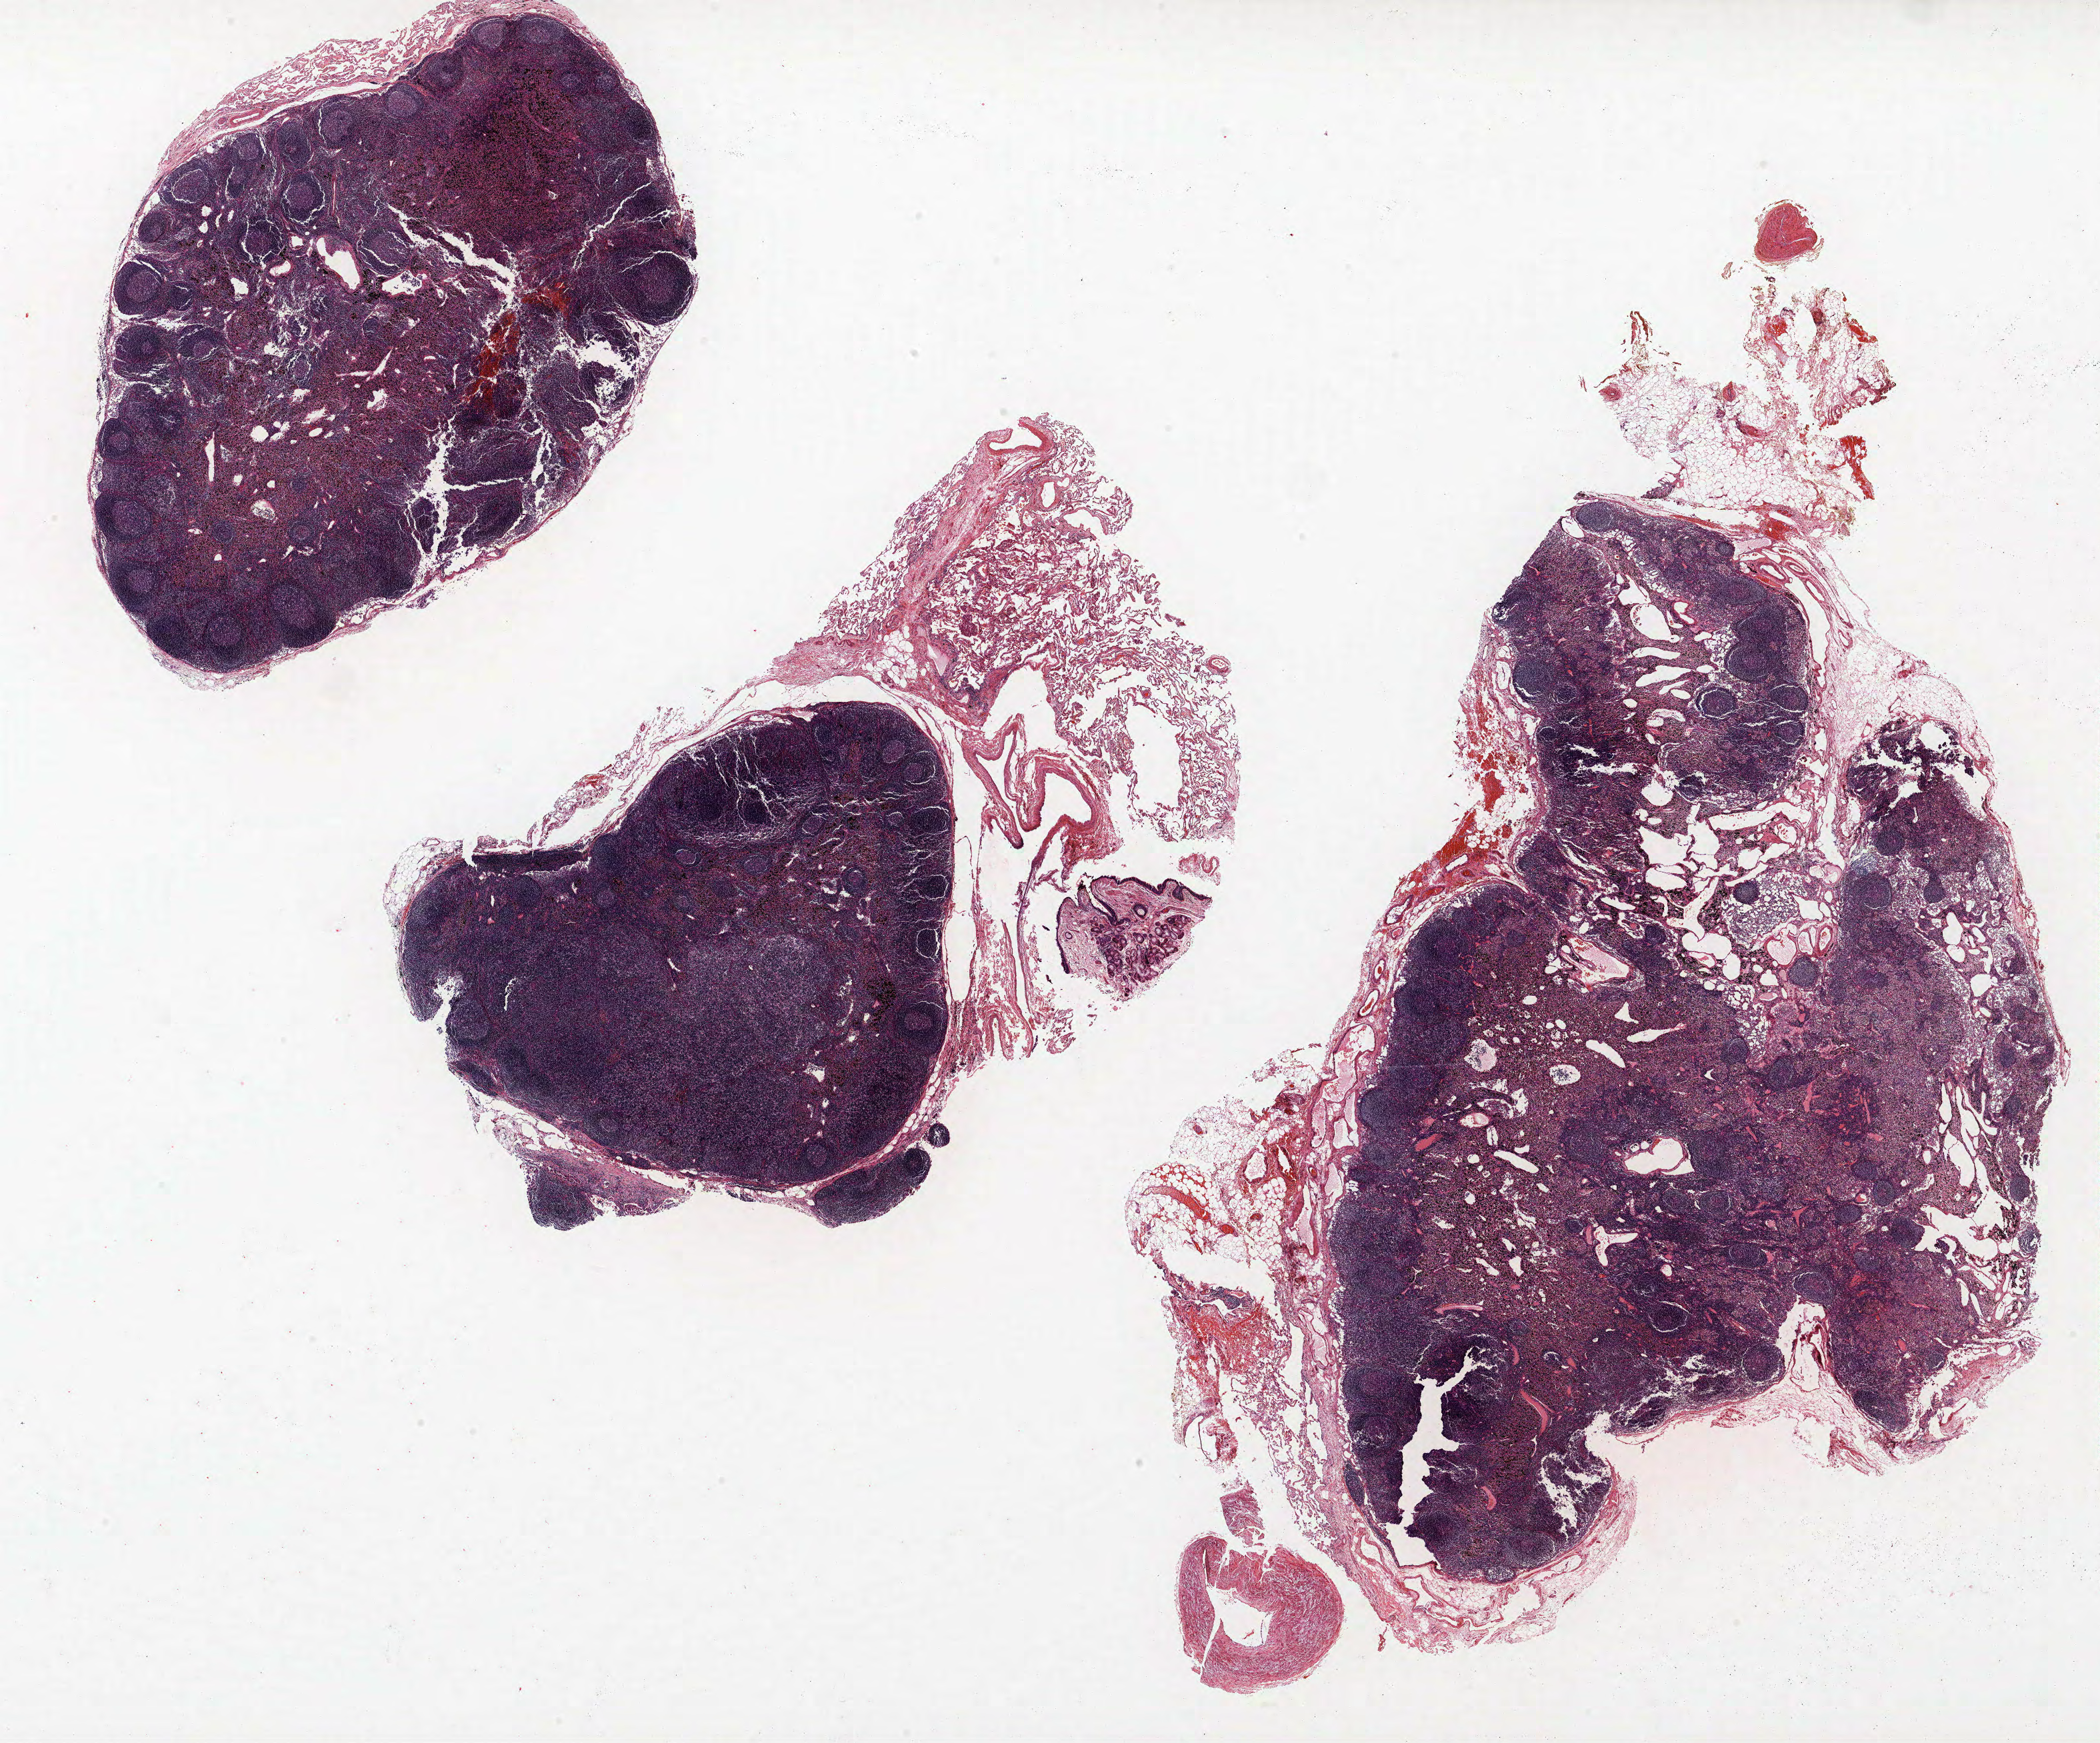
Whole-slide histology image, H&E, a low-resolution overview of the entire scanned area, about 25.2 x 20.9 mm (from a 40x scan). FFPE section. Lung. Female patient, aged 58 at enrolment. Former smoker at enrolment. Grade: poorly differentiated (G3).
ICD-O-3 topography: upper lobe of lung (C34.1). Stage (AJCC 6th edition): IIIA. Primary tumour location (clinical record): left upper lobe. Tumour size (pathology): 37 mm. Participant's lung-cancer diagnosis: Acinar cell carcinoma.